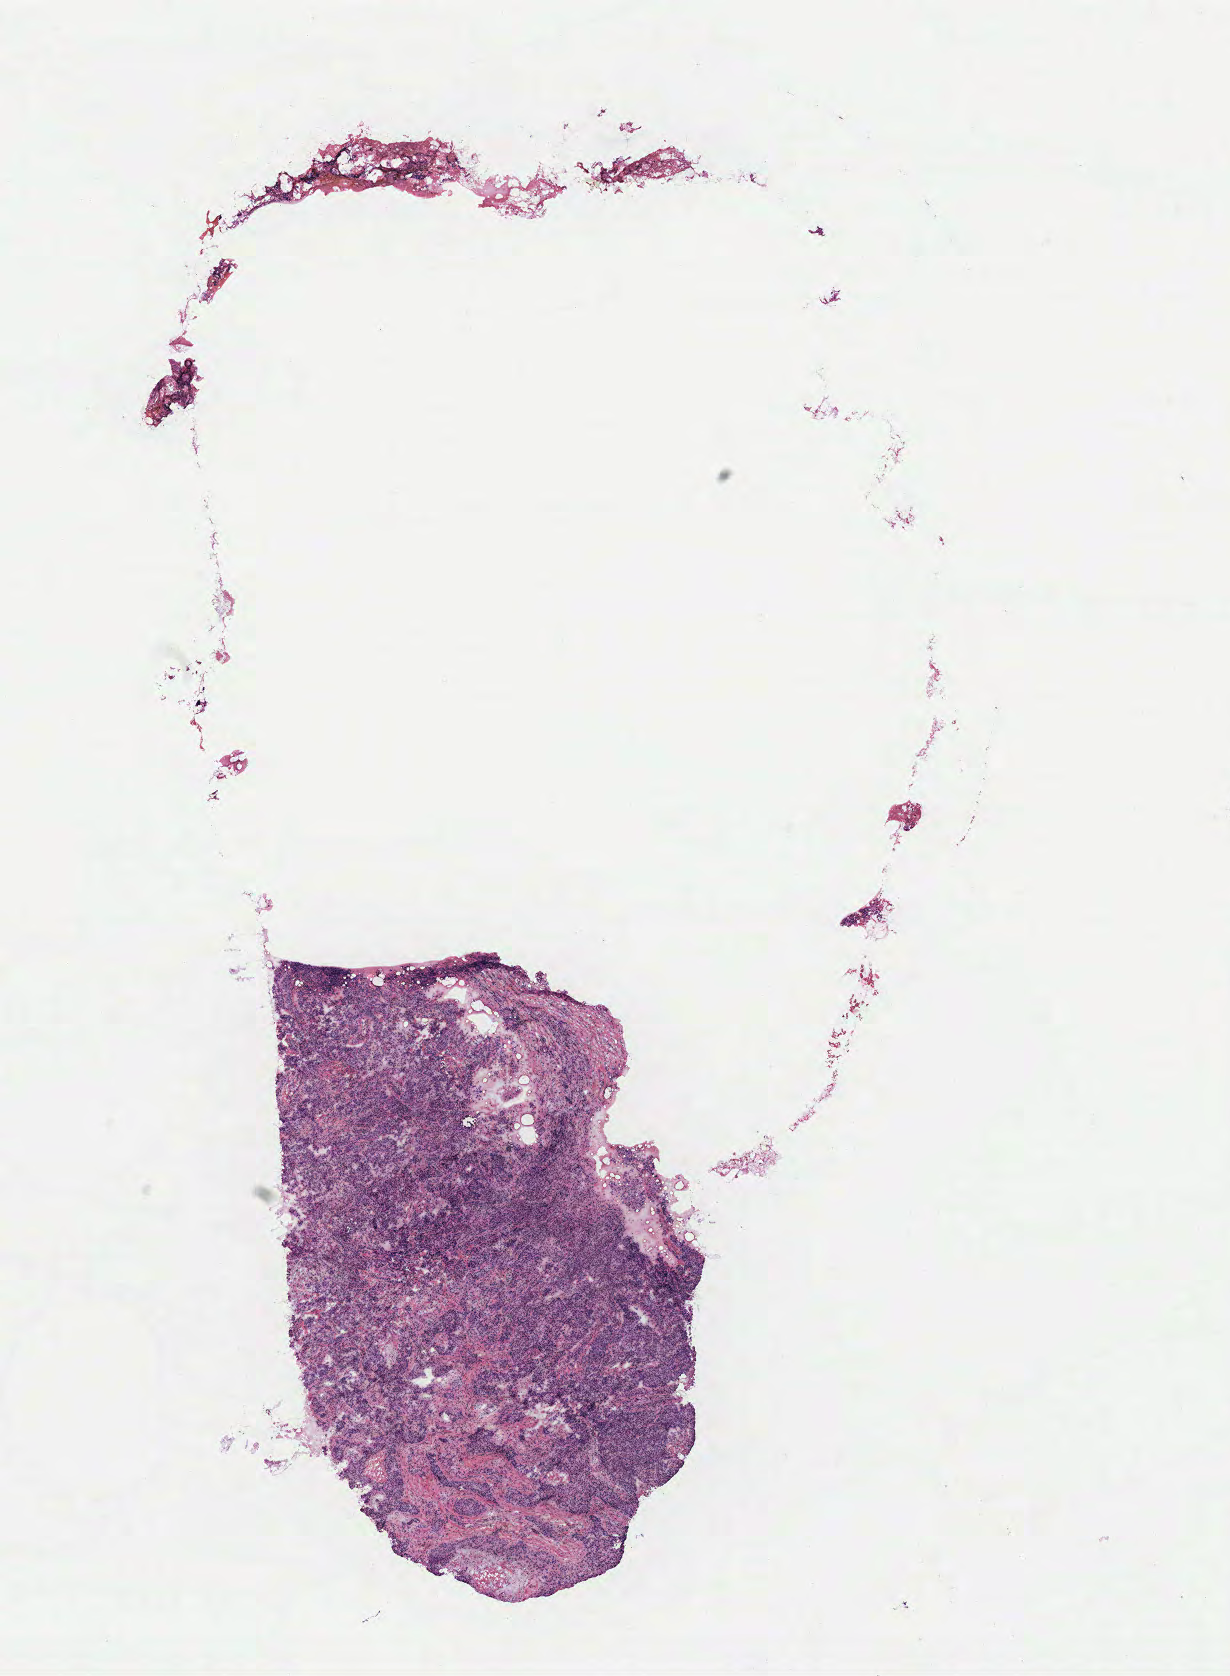
Whole-slide histology image, H&E, whole scanned area (about 9.8 x 13.4 mm, acquisition: 40x scan) shown as a low-resolution overview. Breast, tissue type not recorded.
- patient diagnosis (cohort enrolment): breast cancer (breast)